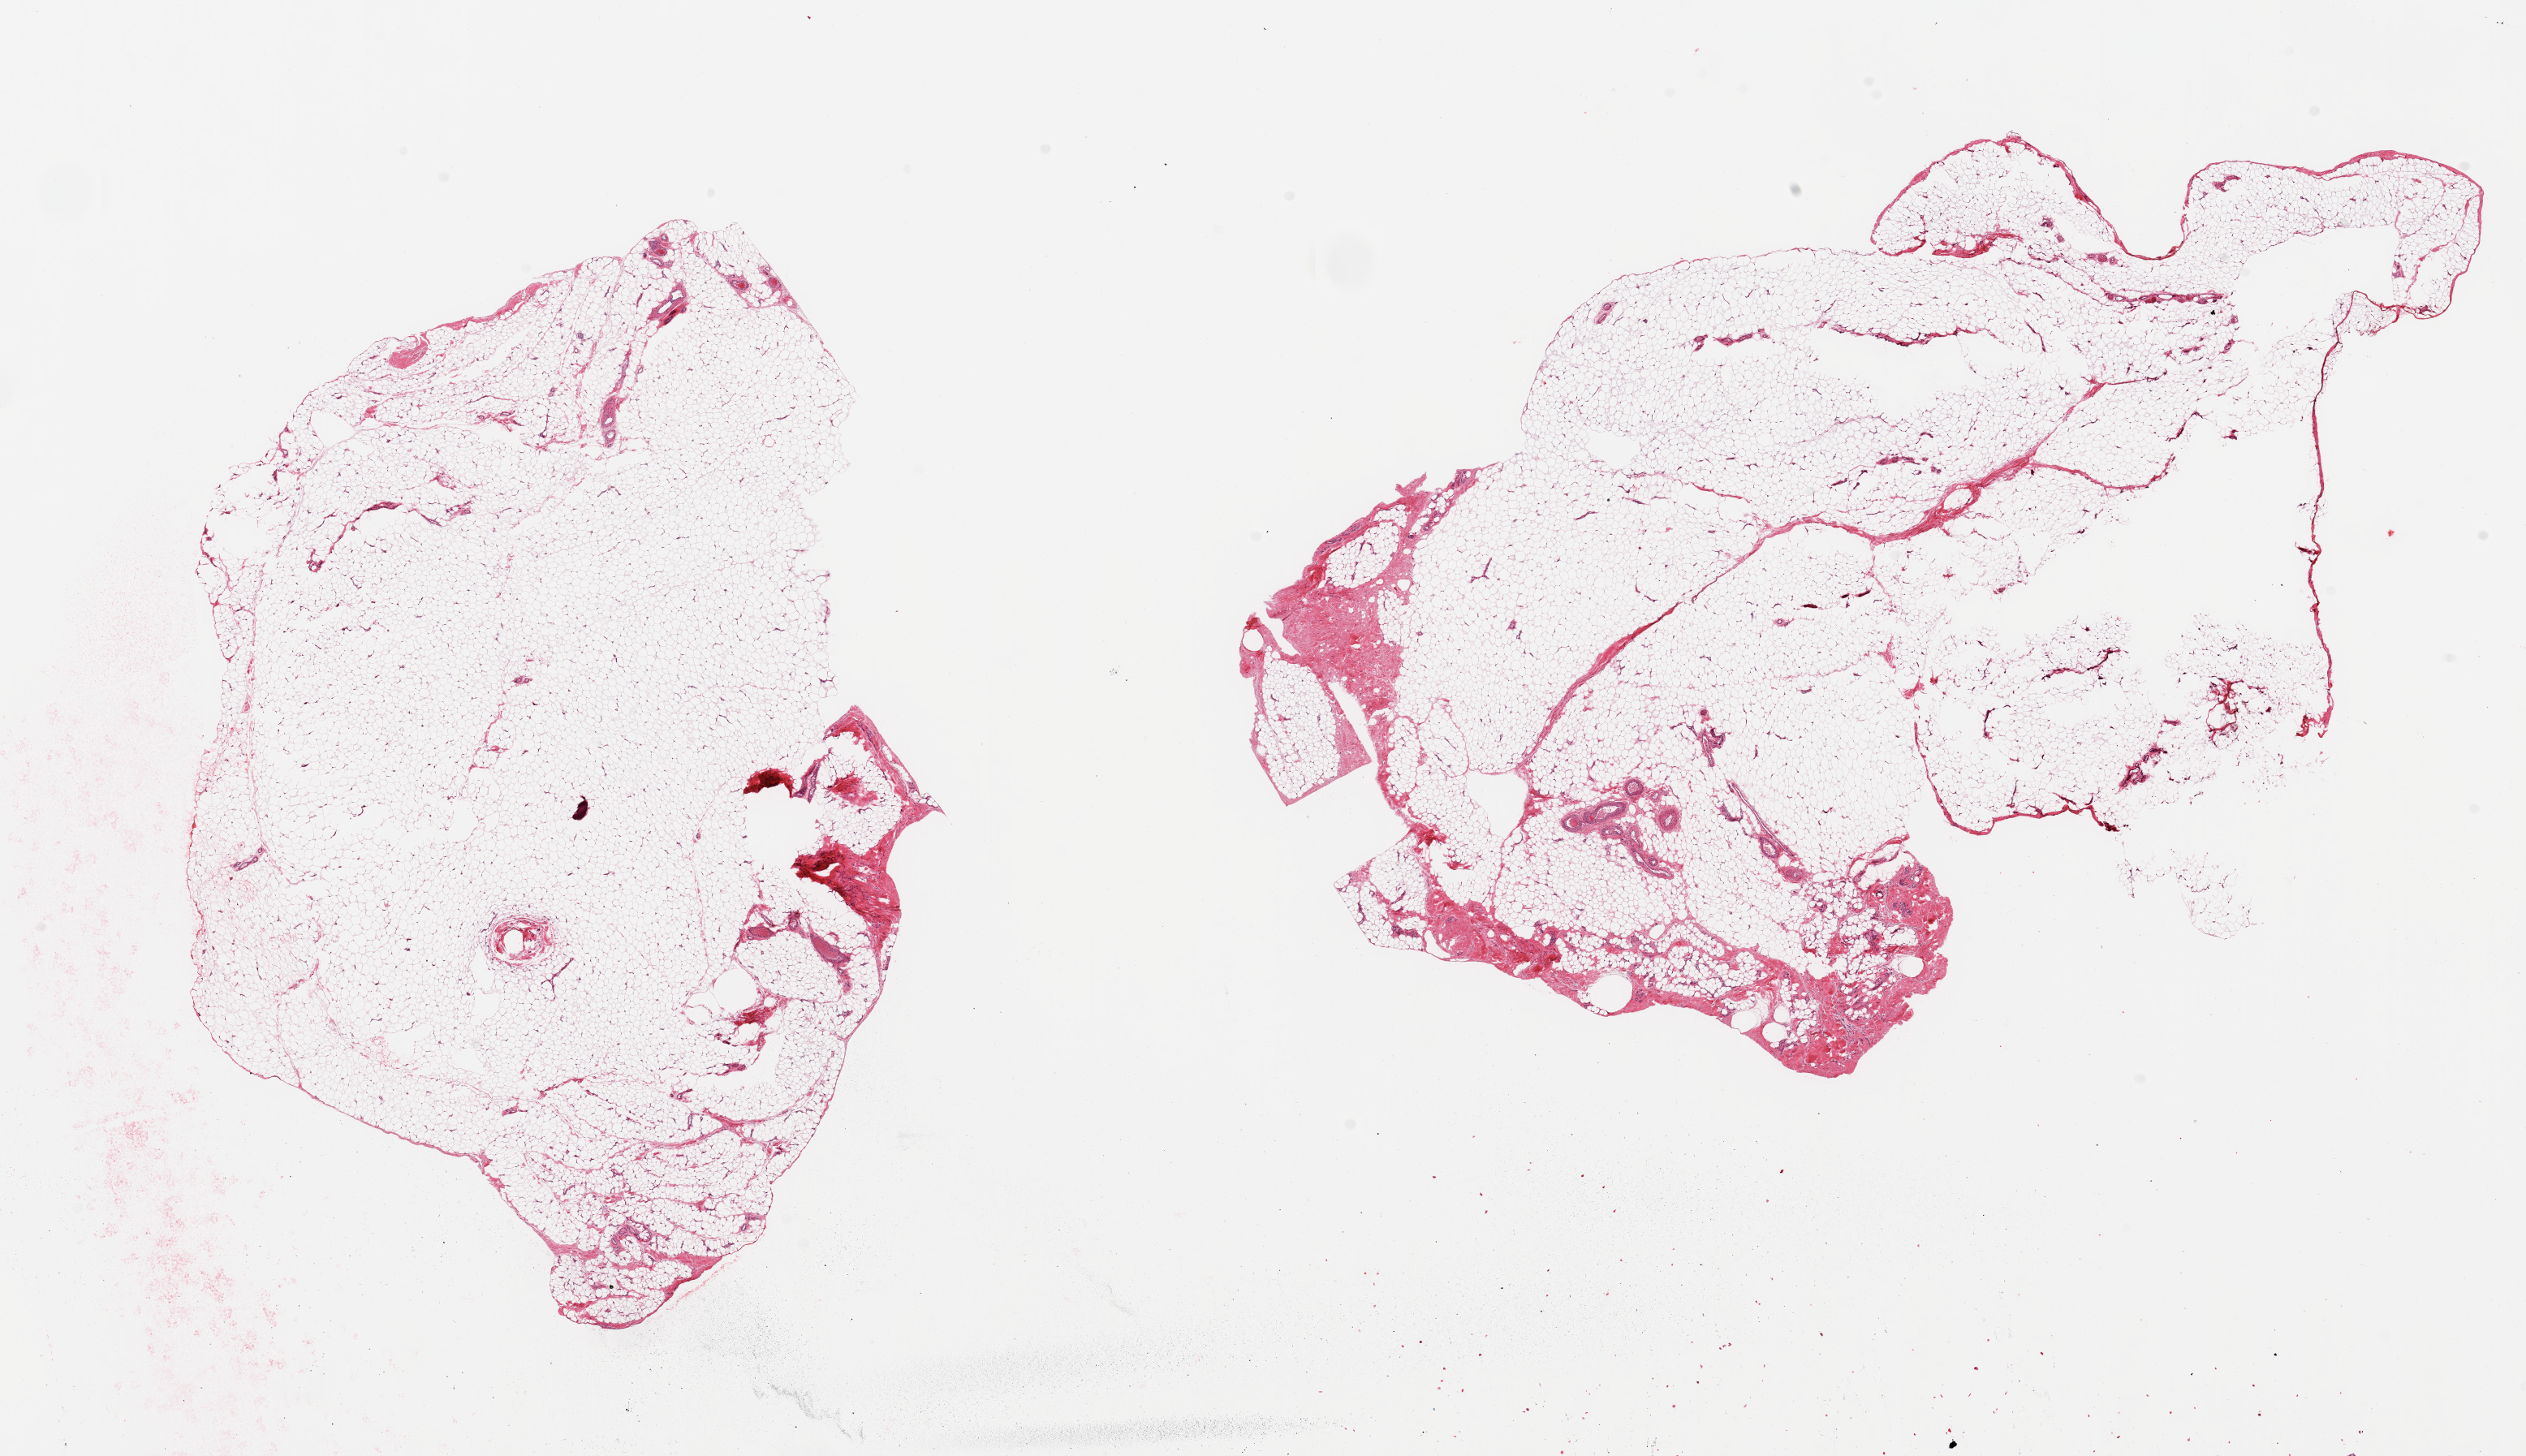
Haematoxylin and eosin whole-slide image — a low-resolution overview of the entire scanned area, about 24.6 x 14.2 mm. PAXgene-fixed paraffin-embedded (PFPE) section. Section of adipose tissue (target tissue). Donor tissue sample. Donor: male.
Review note (as recorded): 2 pieces; some defects in section (oversized), up to 10% fibrous/vascular tissue.